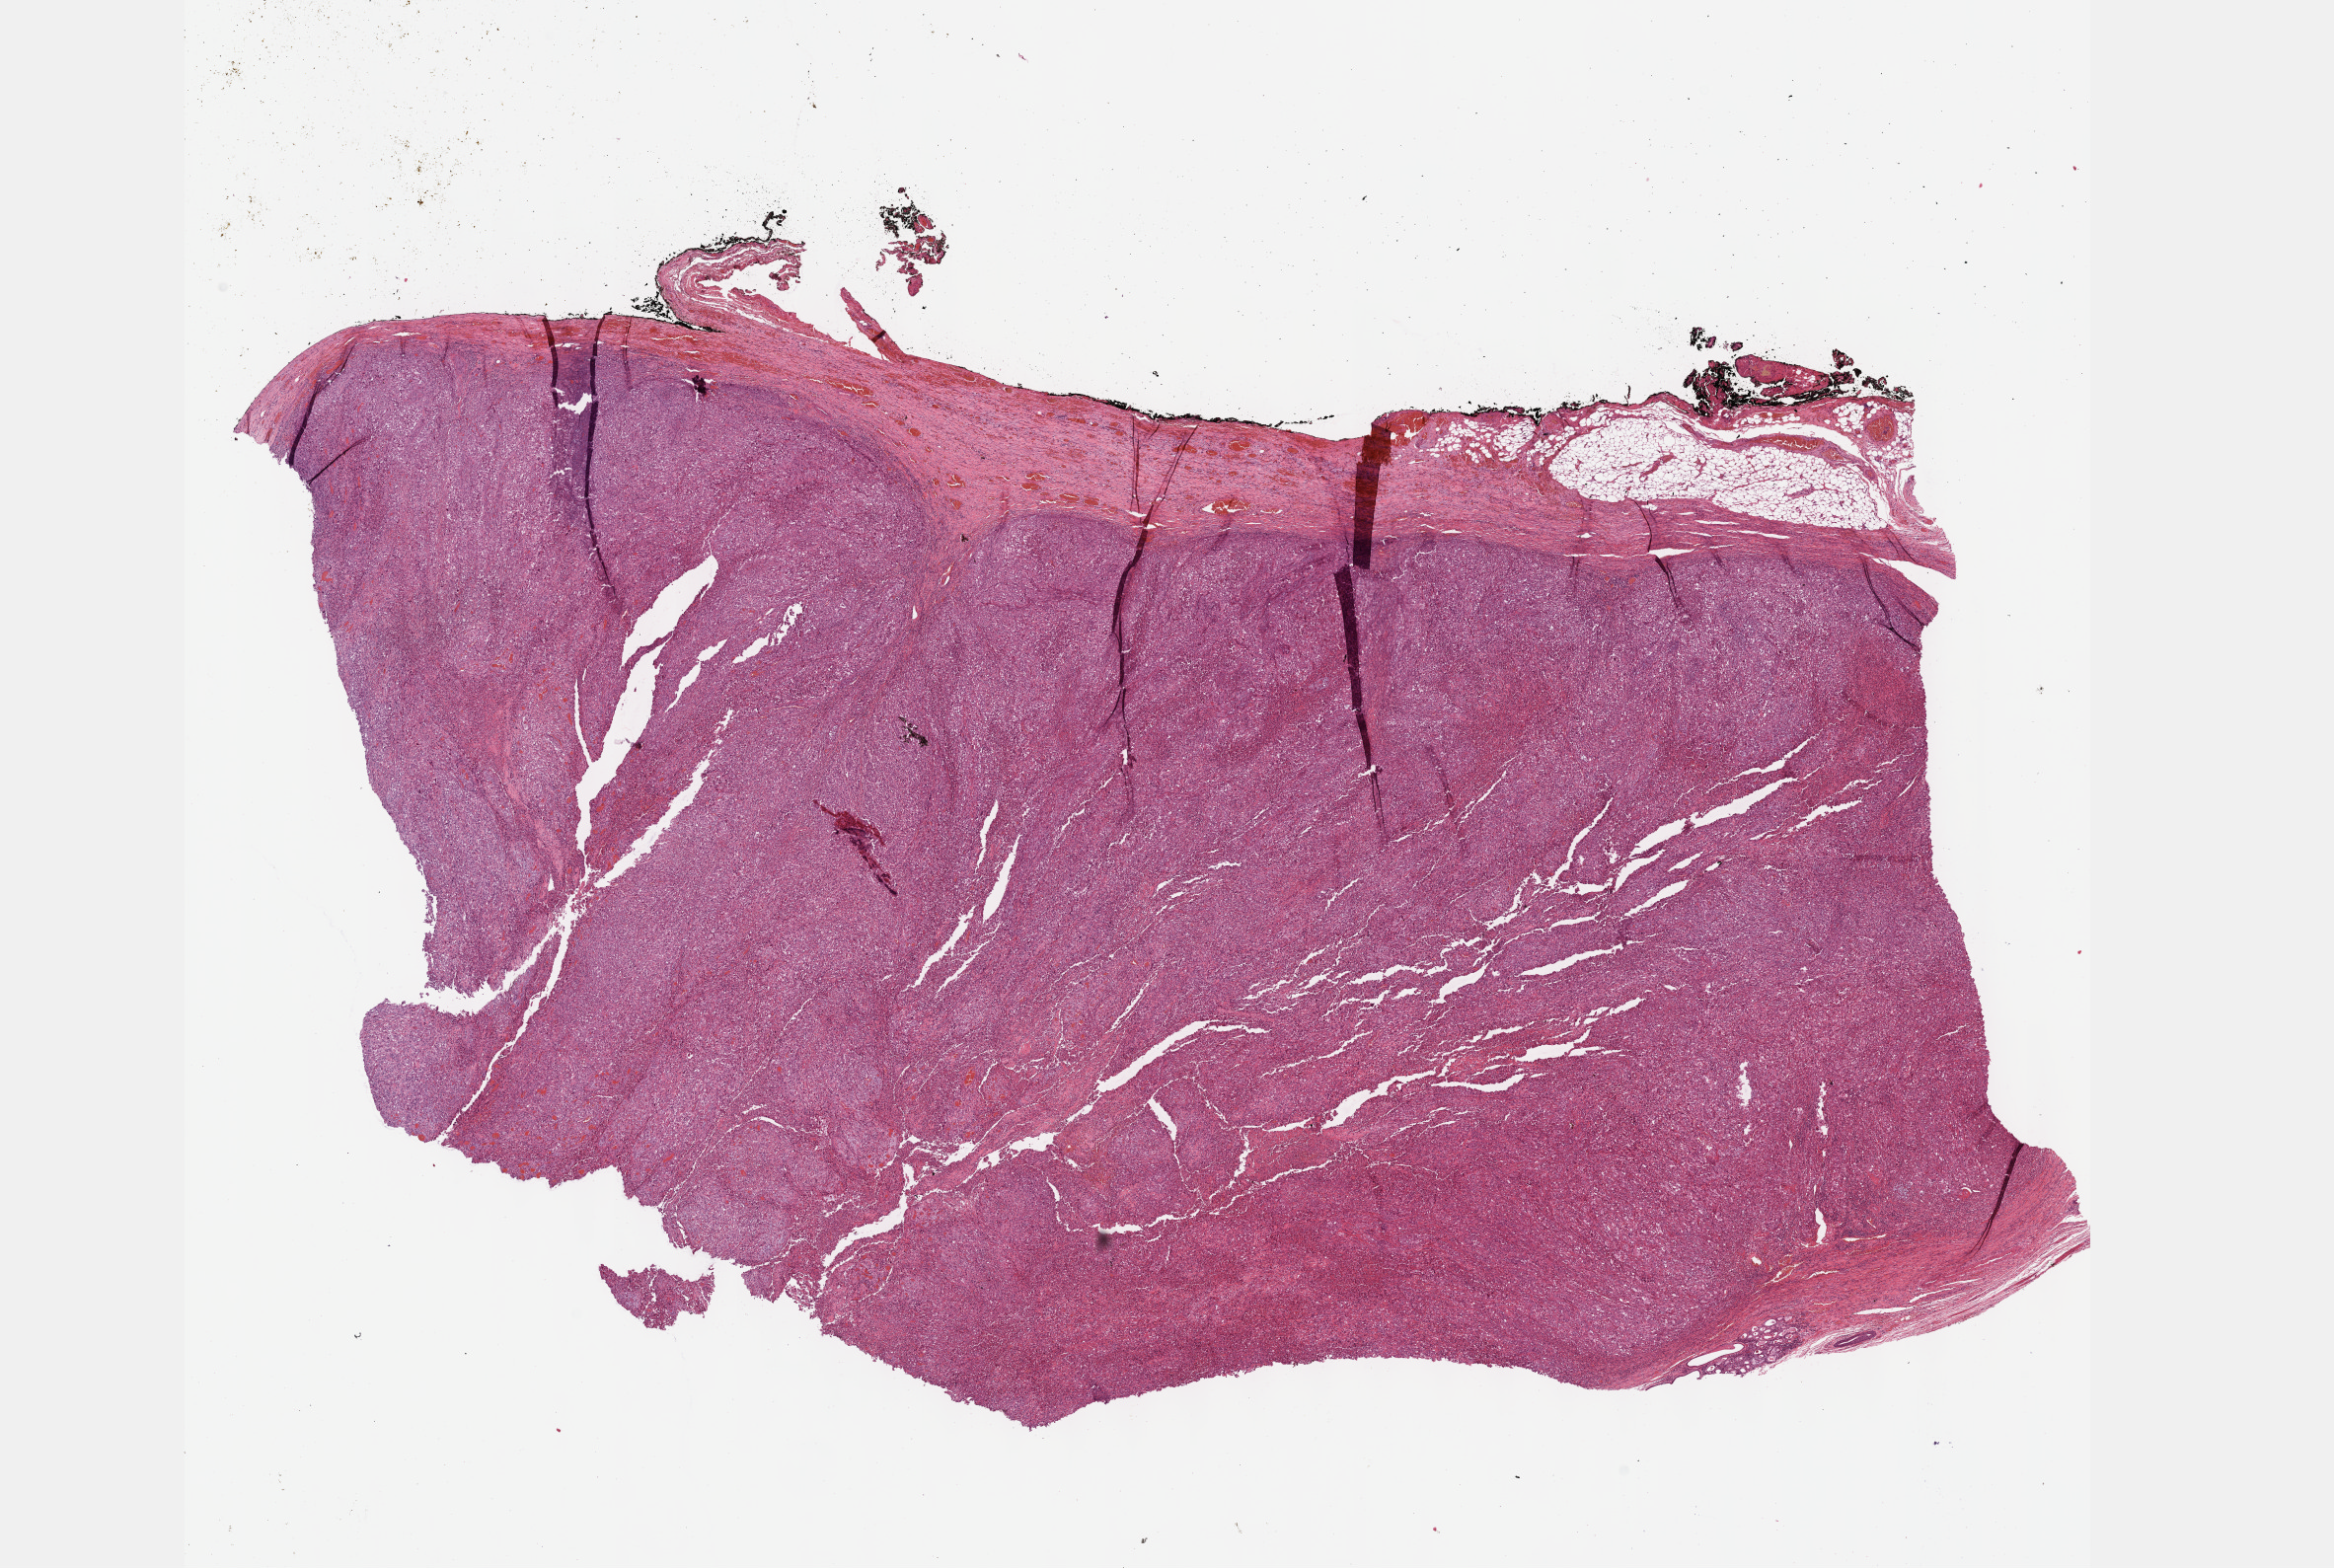
Whole-slide histology image, H&E-stained, whole scanned area (about 19.1 x 12.8 mm, from a 40x scan) shown as a low-resolution overview, formalin-fixed paraffin-embedded (FFPE) diagnostic section, head and neck, primary tumour sample. Female patient; age at initial diagnosis 62 years. Histologic grade: G2 (moderately differentiated).
* AJCC pathologic stage: IVA (7th edition)
* histologic diagnosis: Squamous cell carcinoma, NOS (hypopharynx, NOS)
* laterality: right
* TNM: T4a N2b M0